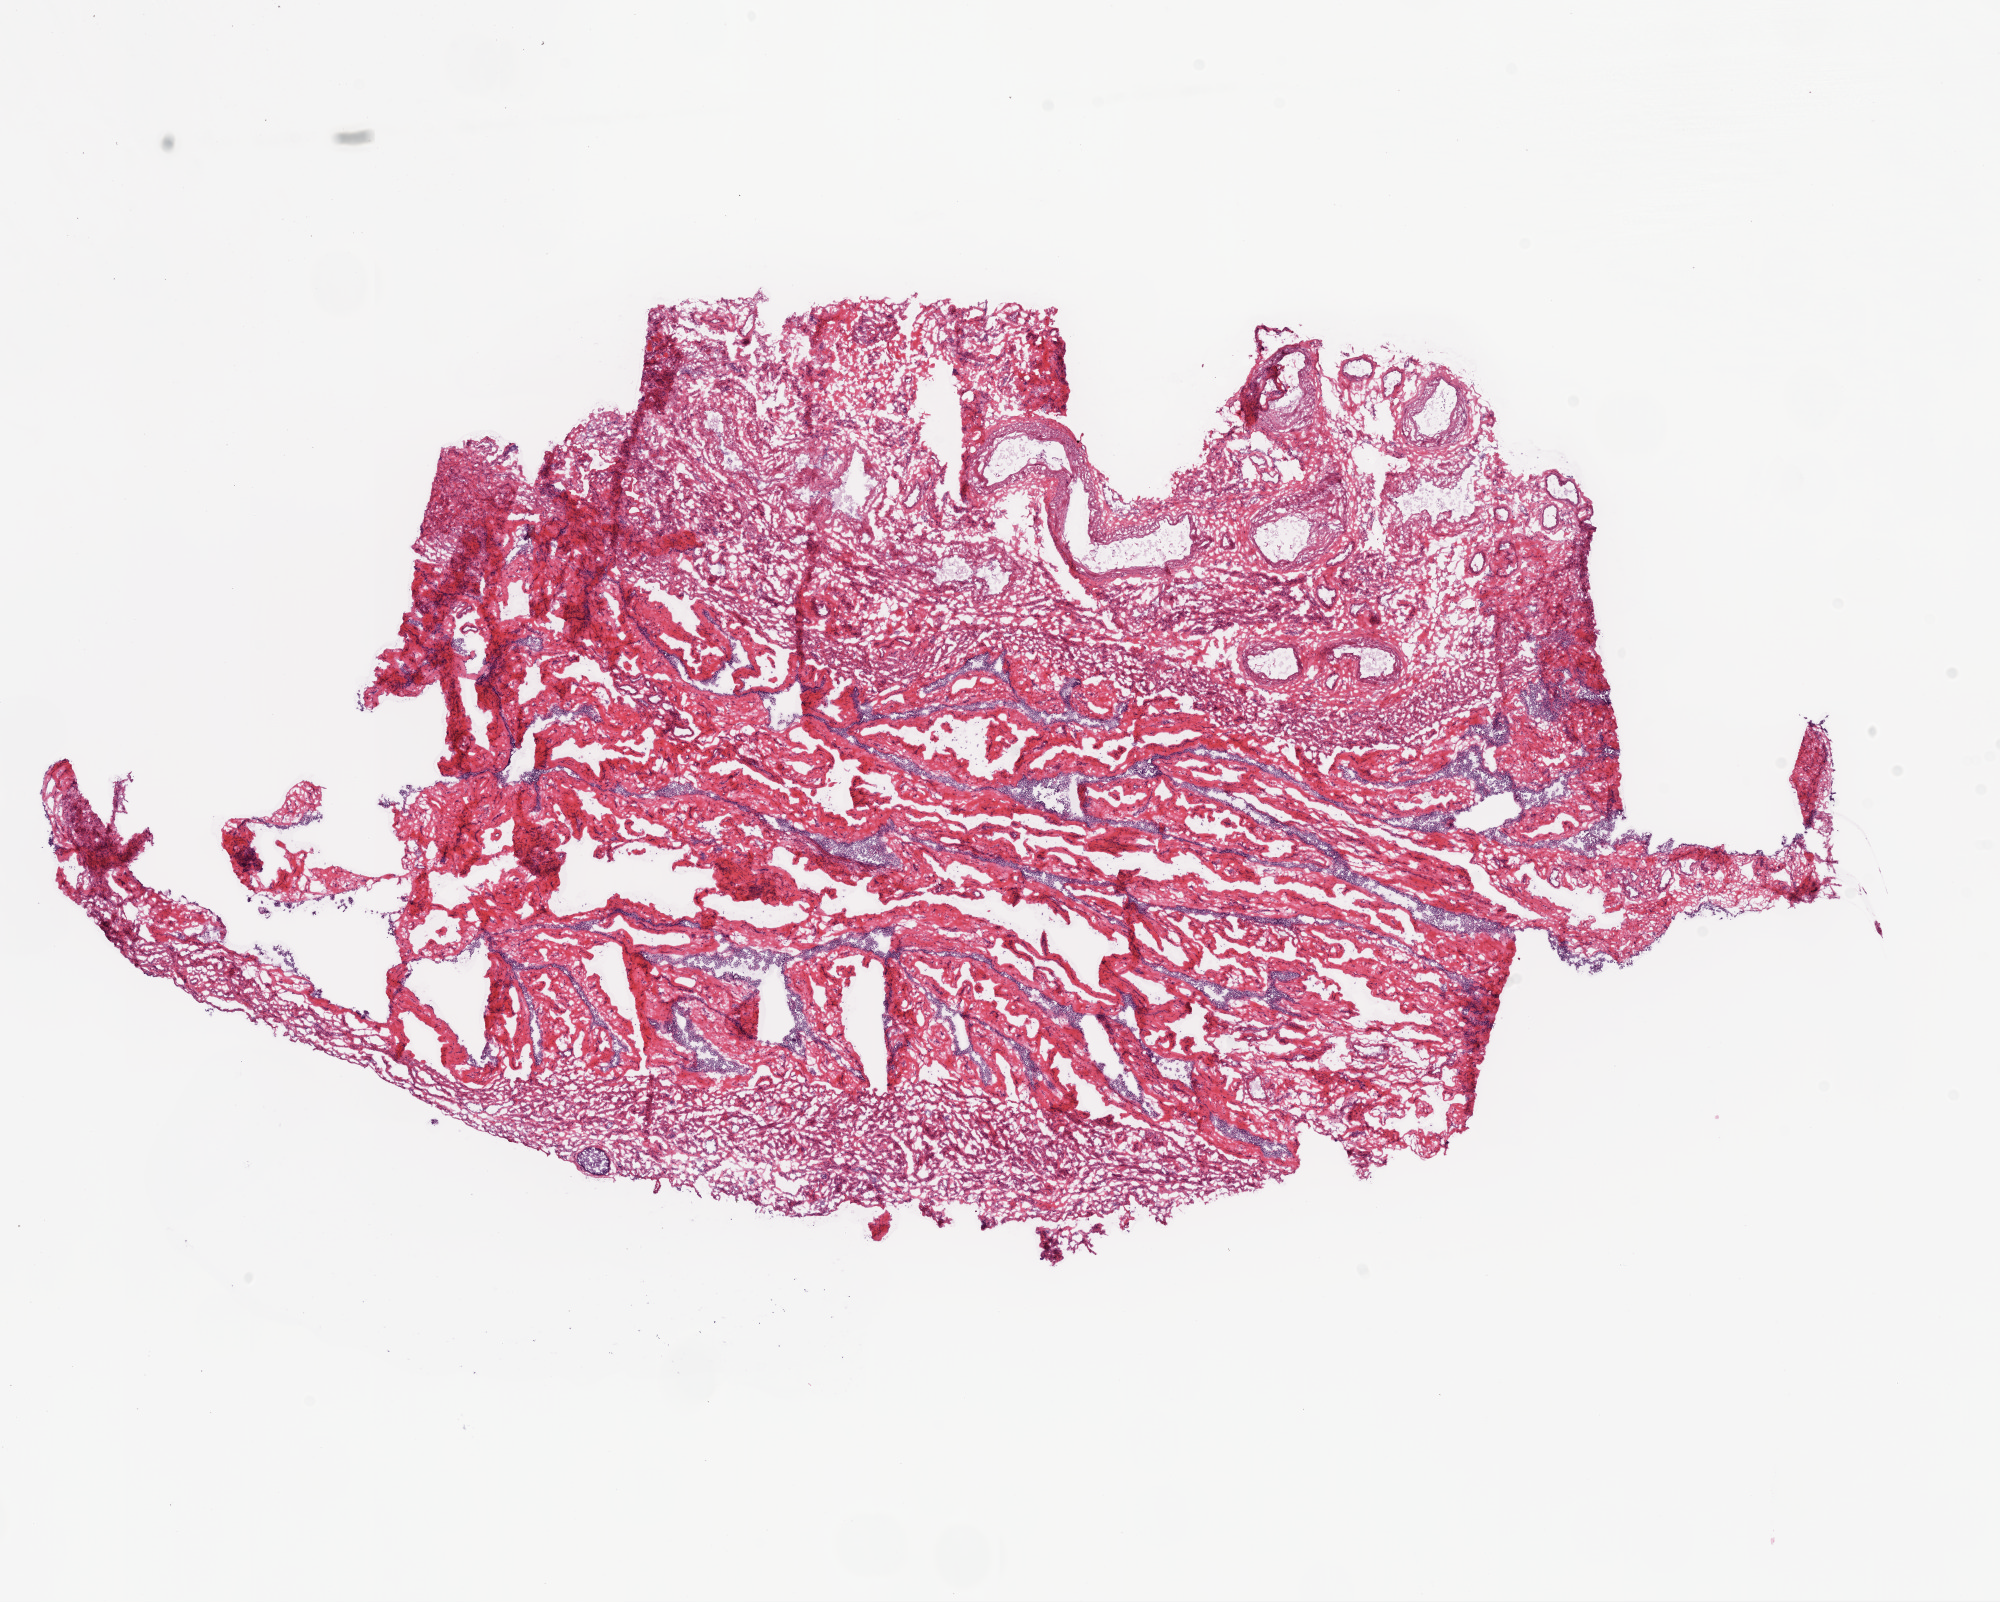
H&E whole-slide image — whole scanned area (about 16.0 x 12.9 mm, slide scanned at 20x) shown as a low-resolution overview; frozen section from the bottom of the tissue portion; ovary, solid tissue normal (non-tumour tissue) sample. Patient: female, age at initial diagnosis 74 years.
This section: solid tissue normal sample (biorepository sample class). Patient diagnosis: Serous cystadenocarcinoma, NOS.